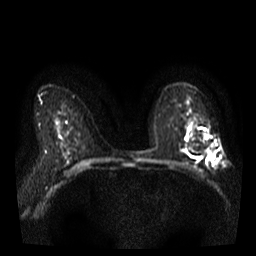
Breast MRI, one axial slice; position 22 of 38 along the scan axis; diffusion-weighted series; image 2 of 4 stored at this slice position (different b-values; order by instance number); 3 T; 5 mm slice thickness; 256 × 256 image matrix. Female patient.
Annotated regions visible in this slice (expert manual segmentation):
- tumour on diffusion-weighted imaging: box from (x=205, y=134) to (x=214, y=165) px